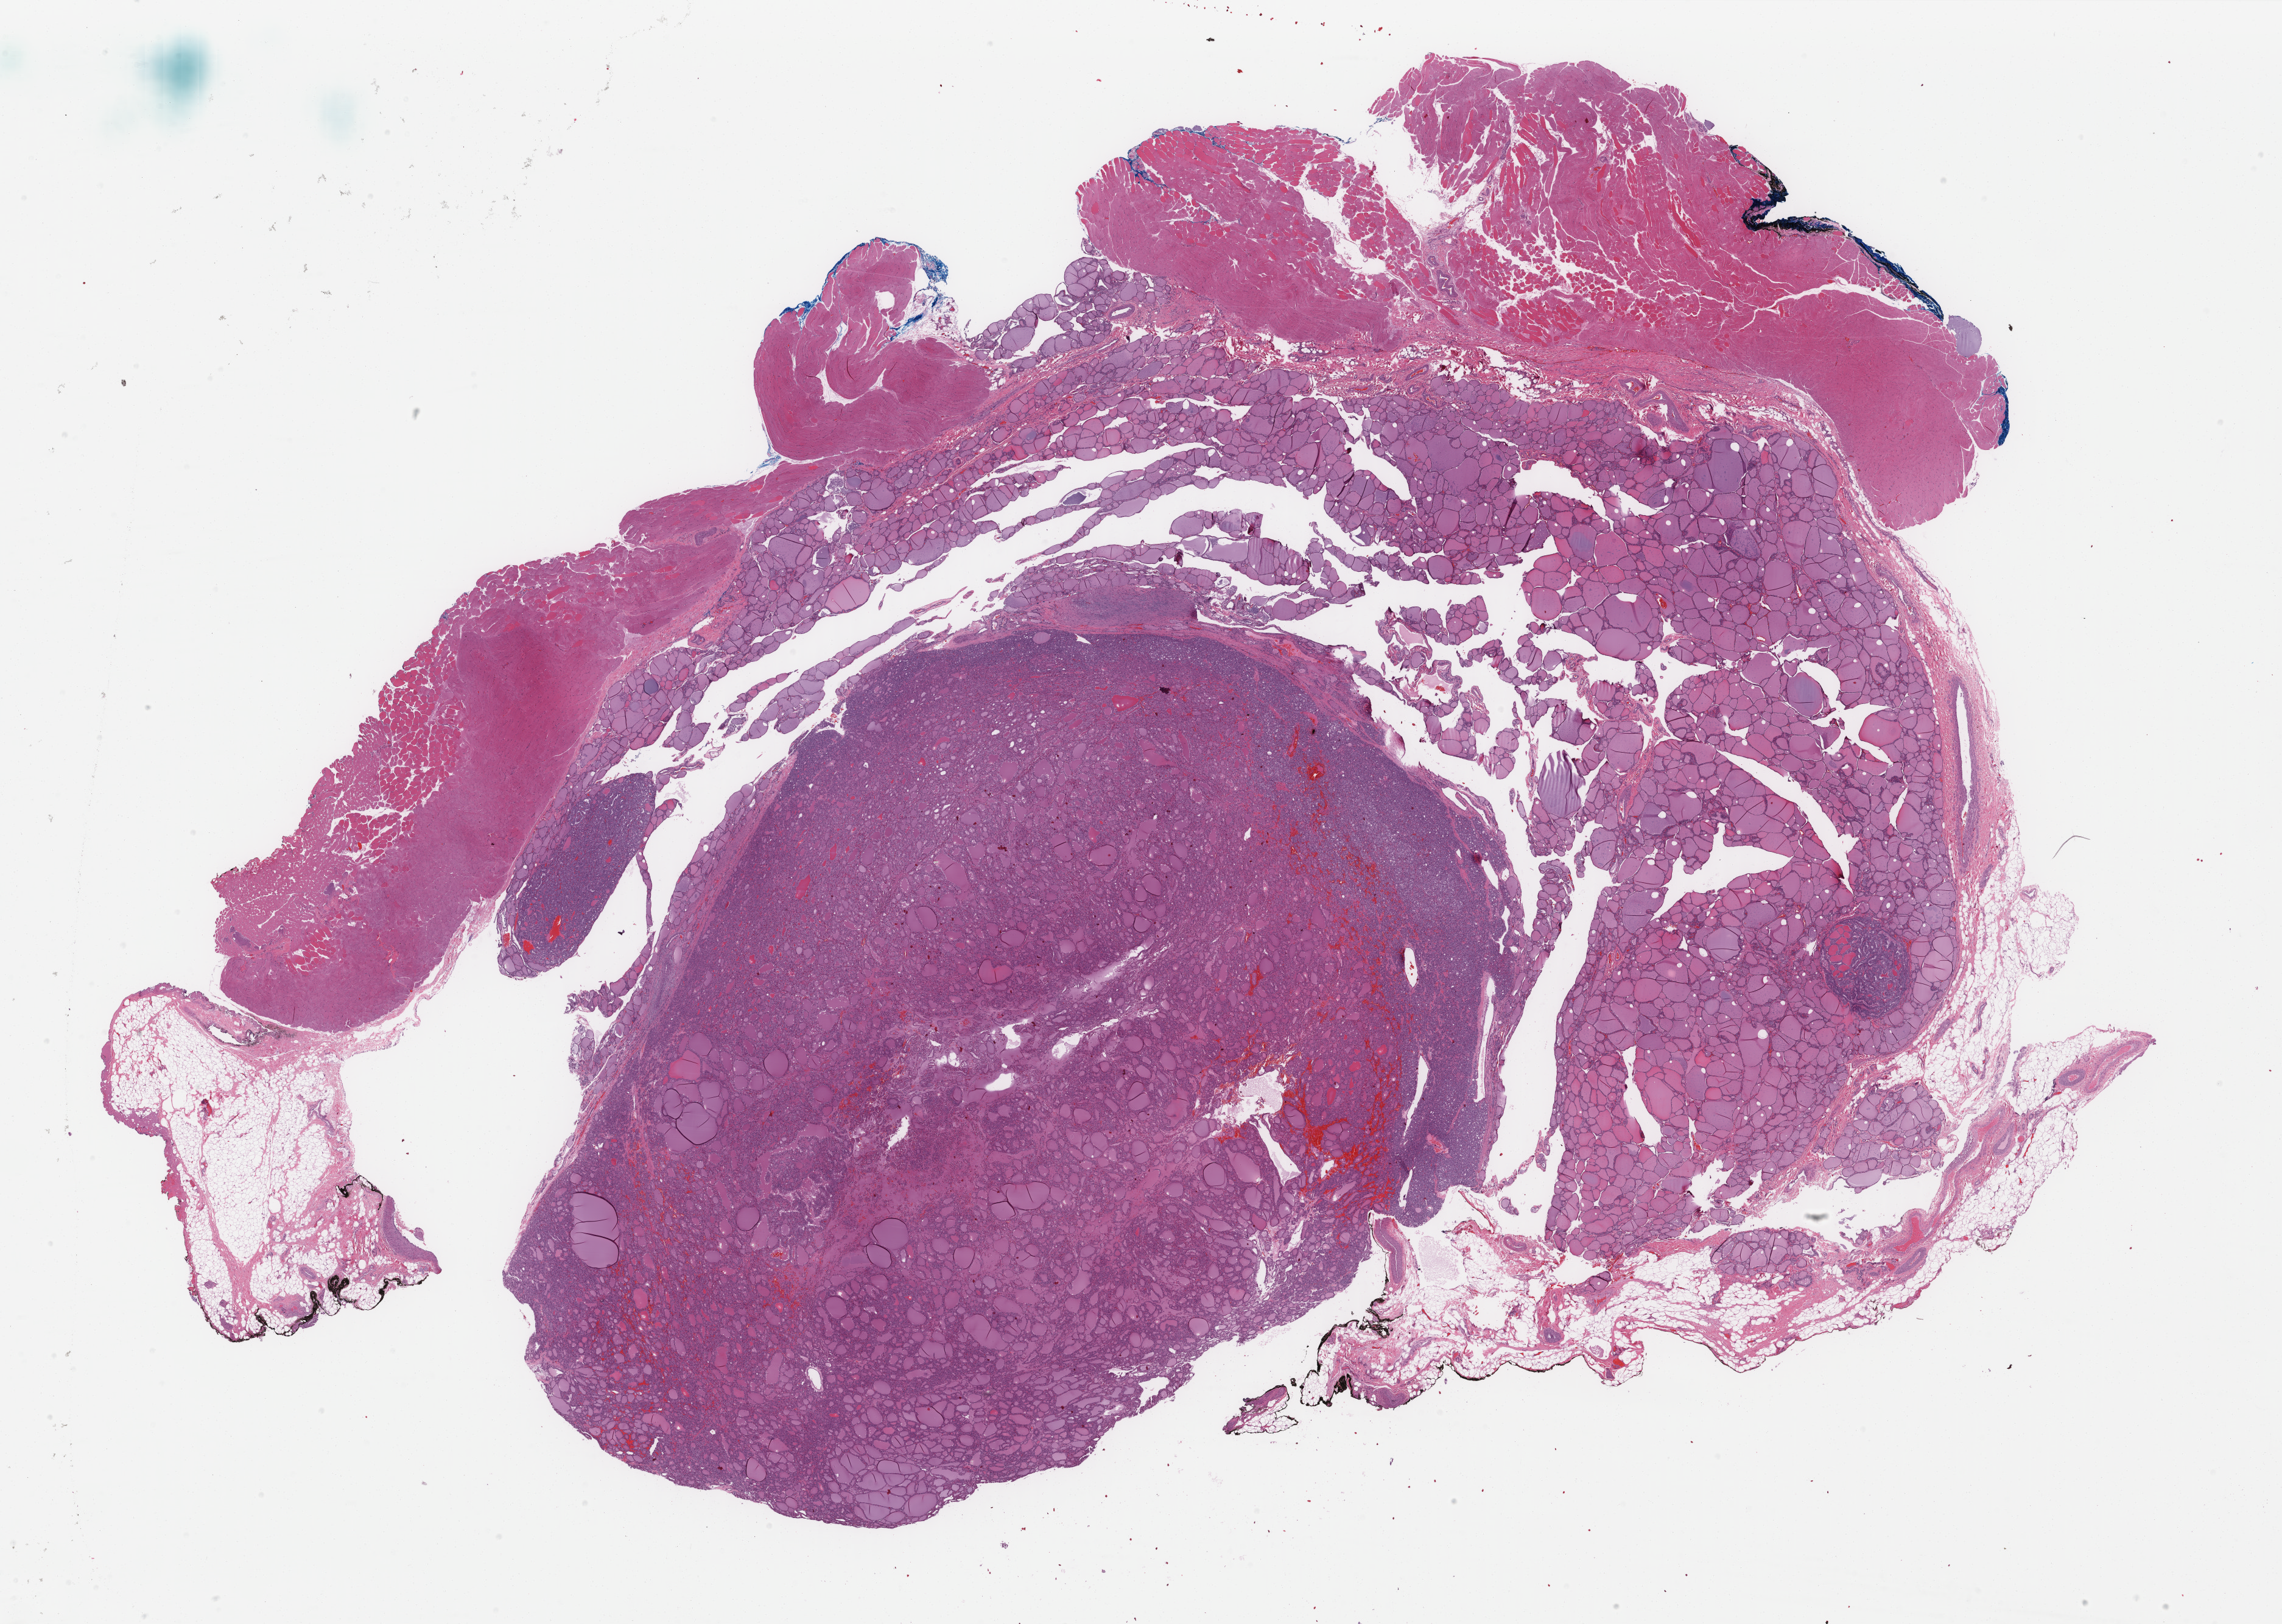
H&E-stained whole-slide image, a low-resolution overview of the entire scanned area, about 29.7 x 21.2 mm (slide scanned at 40x); formalin-fixed paraffin-embedded (FFPE) diagnostic section; sample: primary tumour, thyroid. Female patient; age at initial diagnosis 53 years.
Histologic diagnosis: Papillary carcinoma, follicular variant (thyroid gland). AJCC pathologic stage: IVA (7th edition).